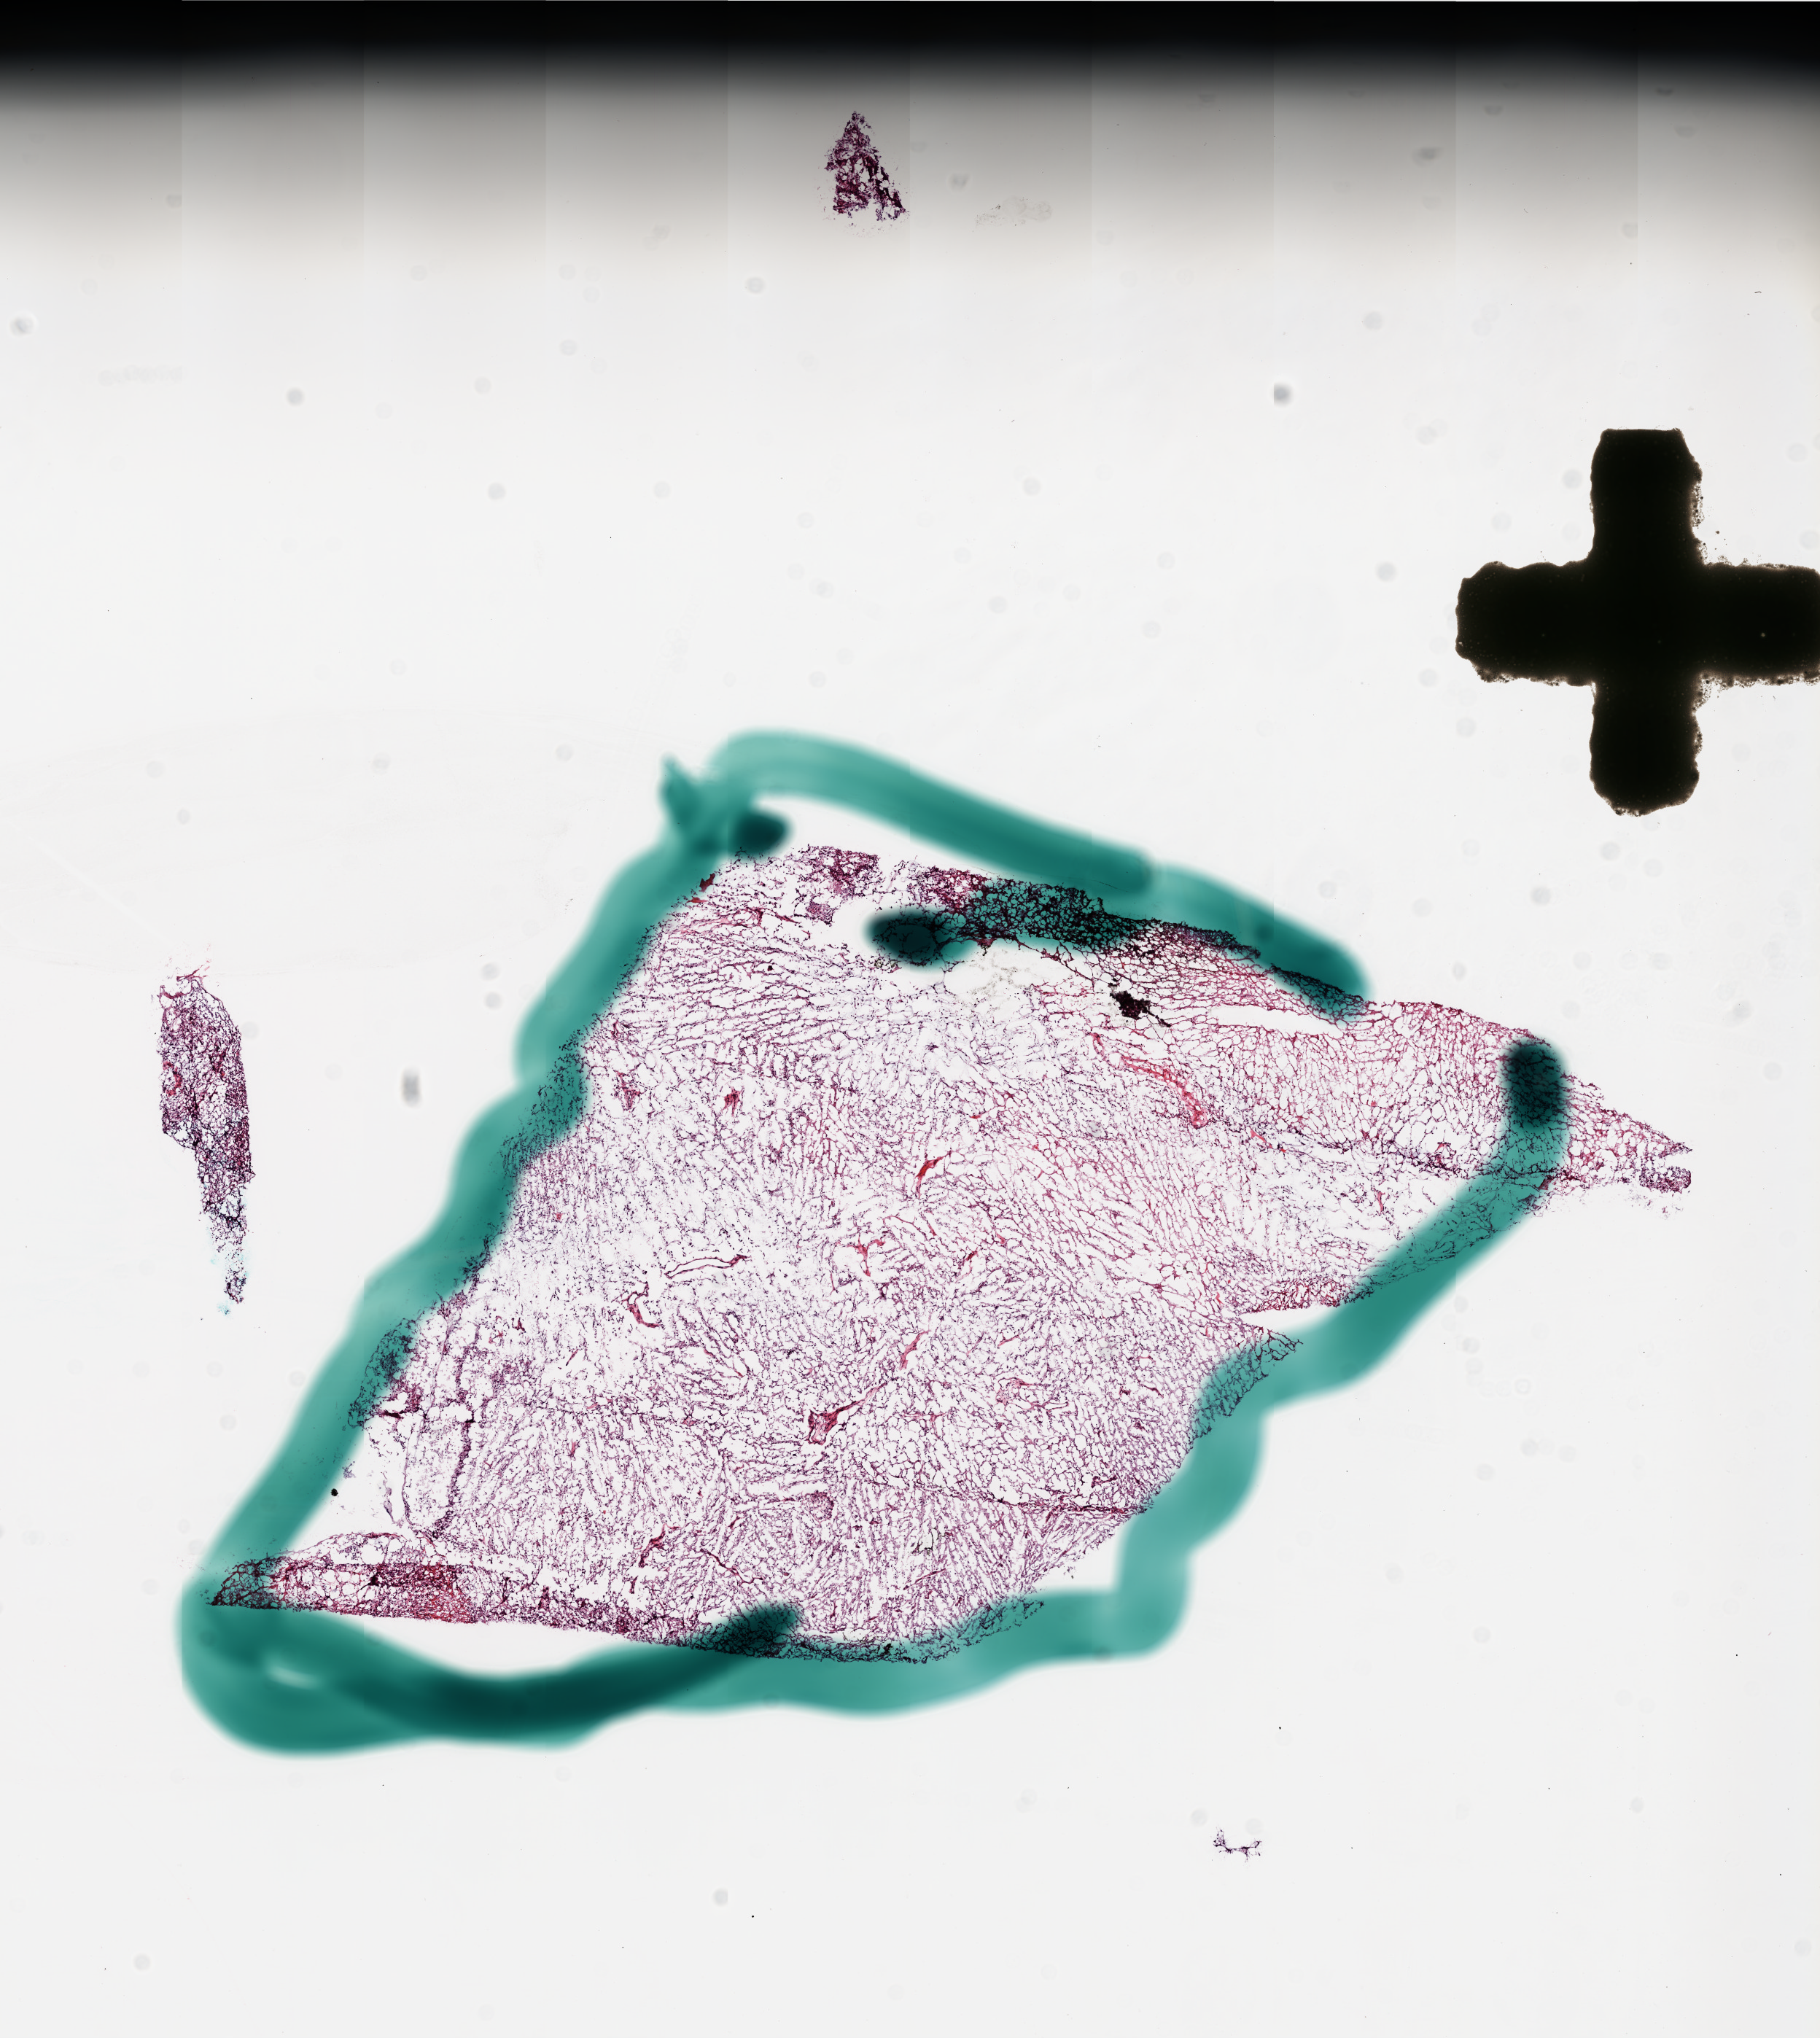
Whole-slide histology image, H&E — whole scanned area (about 10.0 x 11.2 mm) shown as a low-resolution overview, frozen section from the bottom of the tissue portion, brain, primary tumour sample. Male patient; age at initial diagnosis 67 years. Slide review estimates, as recorded: tumour cells 80%, tumour nuclei 100%, normal cells 0%, stromal cells 0%, necrosis 20%.
* diagnosis: Glioblastoma